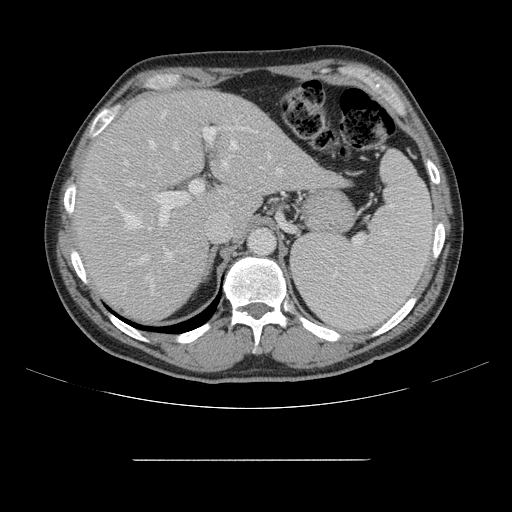
Contrast-enhanced abdominal CT, one axial slice. Slice 106 of 164 in the series (ordered by position). Intravenous contrast given. Soft-tissue window (W 400 / L 40 HU). 2.5 mm slice thickness. 512 × 512 image matrix, field of view 404 × 404 mm. Male patient, age 54 years. From the clinical record (not read from this slice): diagnosis: colorectal cancer liver metastases, imaged before liver resection; multiple liver metastases: yes; largest metastasis: 1 cm.
Structures marked on this image (expert manual segmentation):
- hepatic veins: box from (x=116, y=140) to (x=282, y=278) px
- liver: (x=76, y=91)–(x=341, y=322)
- planned liver remnant (the part of the liver to remain after resection): (x=77, y=91)–(x=240, y=322)
- portal vein (with intrahepatic branches): (x=120, y=111)–(x=252, y=296)